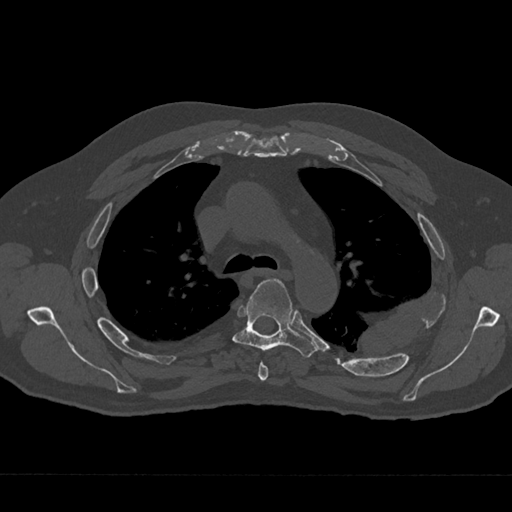
CT including the spine, one axial slice. Position 482 of 797 along the scan axis. 120 kVp. Bone window (W 1800 / L 400 HU). 0.5 mm slice thickness. 512 × 512 image matrix, field of view 377 × 377 mm. Male patient, age 75 years. Case-level facts recorded for this patient, not image findings: primary cancer: renal; vertebrae with lytic lesions (as recorded): T4.
Outlined on this slice (semi-automatic segmentation, software-assisted and operator-edited):
- T4 vertebra: bounding box [x1, y1, x2, y2] px = [258, 362, 269, 381]
- T5 vertebra: [232, 278, 317, 358]